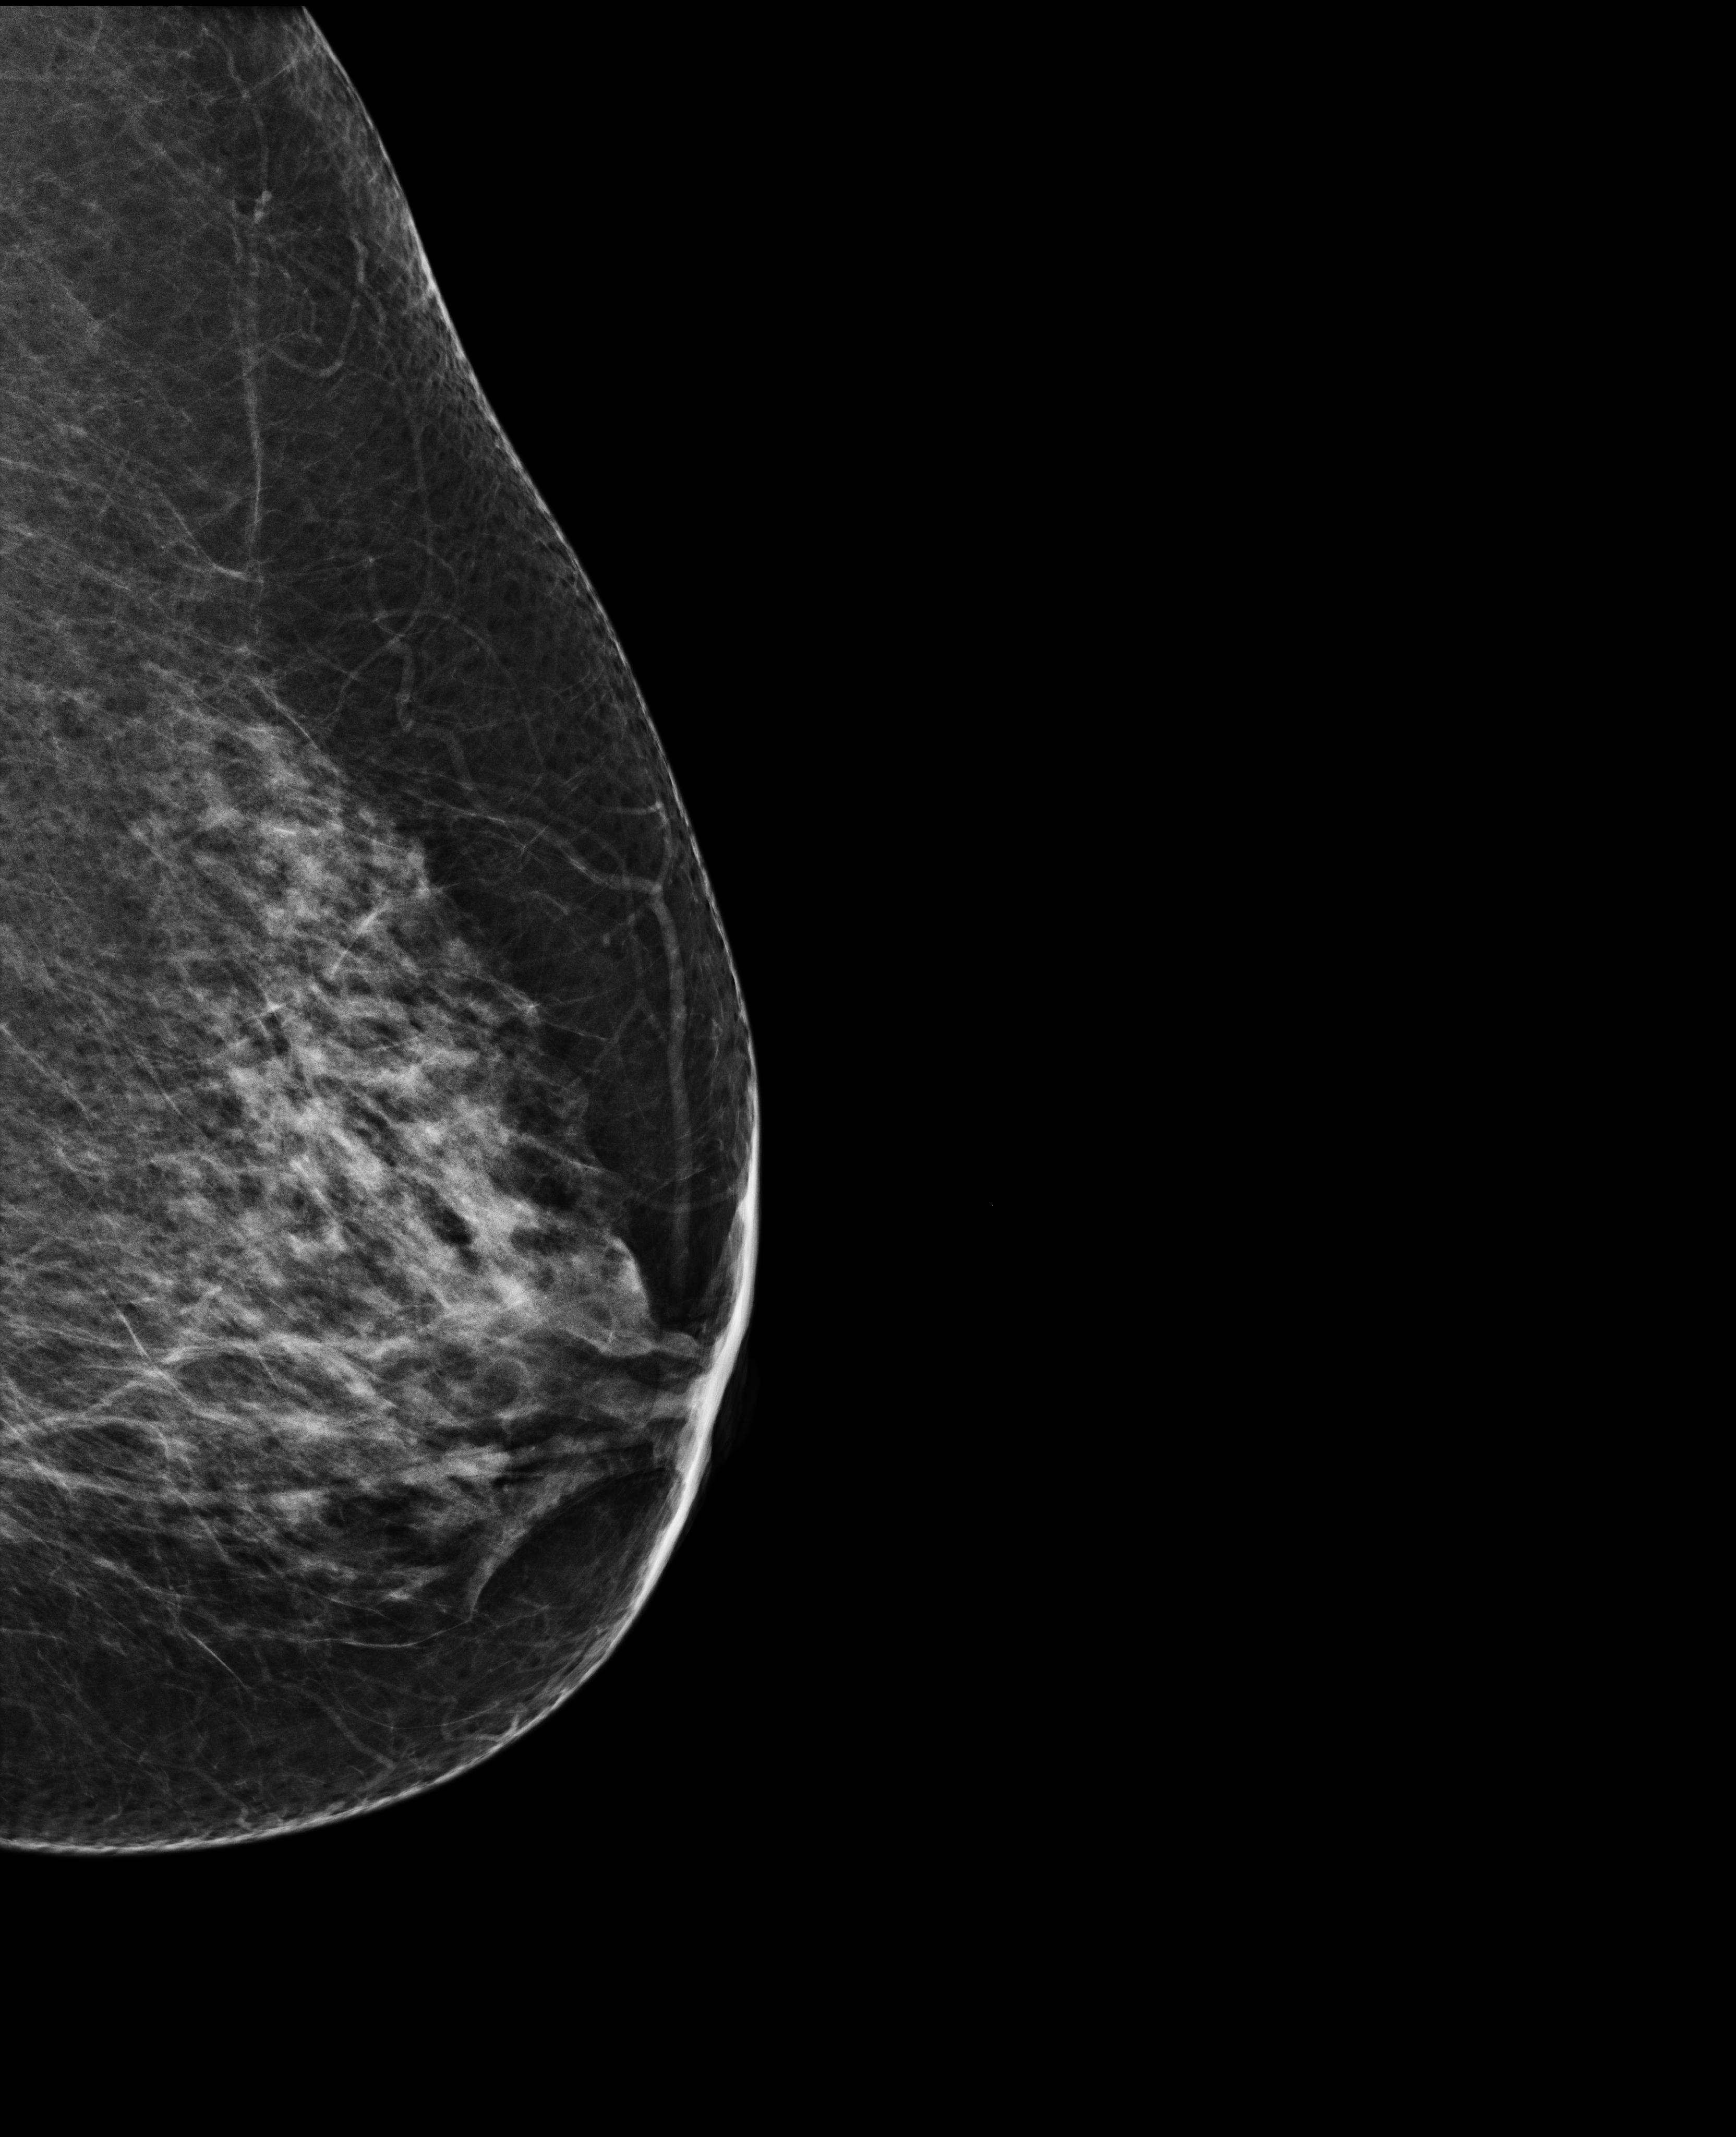
Full-field digital mammogram (FFDM), left breast, laterally exaggerated craniocaudal (XCCL) view, screening examination, compressed breast thickness 67 mm, system: Selenia Dimensions. Patient aged 71 years (female).
BI-RADS breast density category at the screening exam (both breasts, scale 1–4): 3. Final BI-RADS assessment for this screening round (tomosynthesis exam, both breasts): category 2. Recall: no recall after this screen.